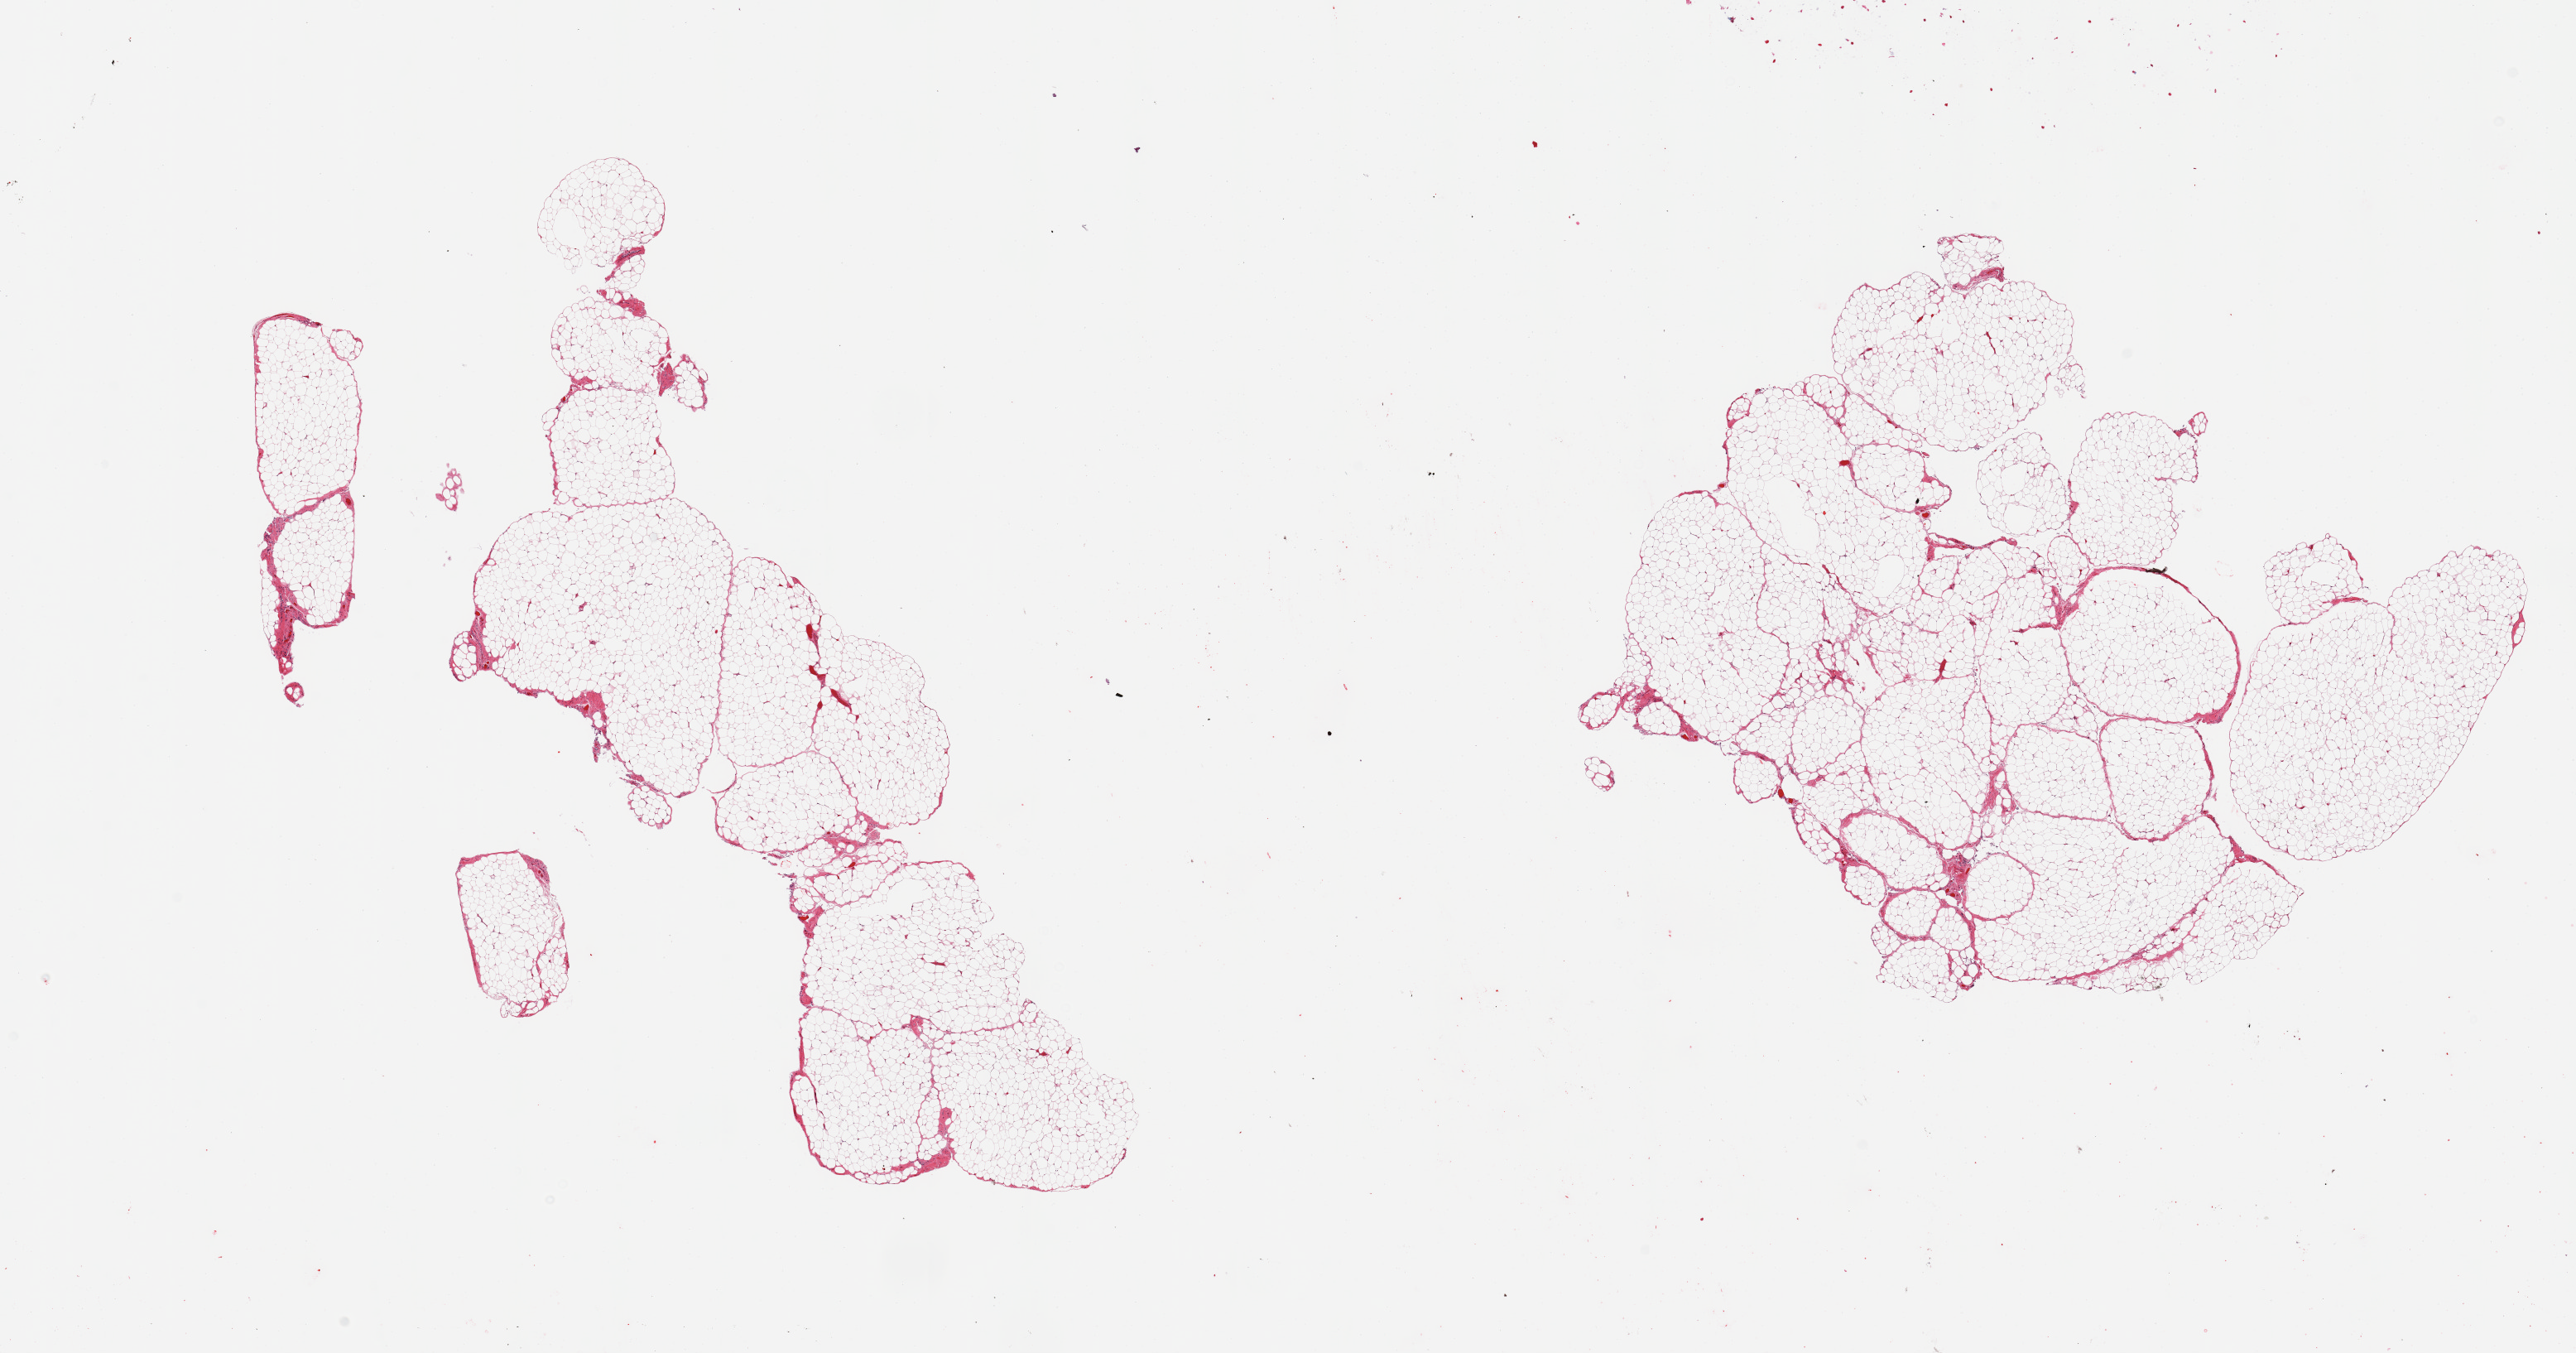
Hematoxylin and eosin (H&E) whole-slide image, a low-resolution overview of the entire scanned area, about 24.6 x 12.9 mm; PAXgene-fixed, paraffin-embedded tissue; target tissue: omentum; tissue donor sample. Male donor.
Reviewer comment on this tissue sample: 2 pieces; focally fragmented mature adipose tissue with 5% fibrovascular septa.